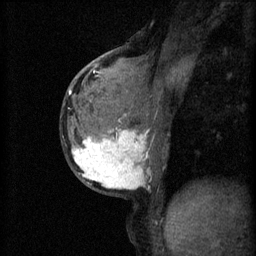
Breast MRI (dynamic contrast-enhanced), one sagittal slice; 3 images stored at this slice position (order not interpretable as contrast timing); 1.5 T; TE 4.2 ms, TR 11 ms; 2 mm slice thickness; 256 × 256 image matrix, field of view 180 × 180 mm. Female patient, age 37 years.
Outlined on this slice (semi-automatic segmentation, software-assisted and operator-edited):
- analysis volume of interest (the breast-tissue region the enhancement analysis was run in; not a lesion): bounding box <68,118,159,195> (left, top, right, bottom; pixels)
- tumour enhancement mask (voxels above the 70 % enhancement threshold inside the analysis volume of interest): <72,128,148,189>